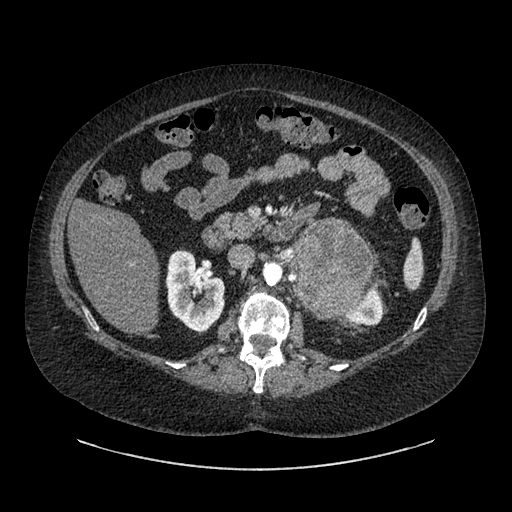
Contrast-enhanced abdominal CT, one axial slice. Position 526 of 769 along the scan axis. Reconstruction kernel SOFT. Intravenous contrast given. Soft-tissue window (W 400 / L 40 HU). 0.62 mm slice thickness. 512 × 512 image matrix. Patient: female, 61 years. From the clinical record (not read from this slice): diagnosis: adrenocortical carcinoma; tumour side: left adrenal; tumour size at pathology: 13 cm; Ki-67 index: 79 %; stage (as recorded): 2.
Structures marked on this image (semi-automatically segmented with operator editing):
- mass: bounding box [x1, y1, x2, y2] px = [294, 223, 378, 312]